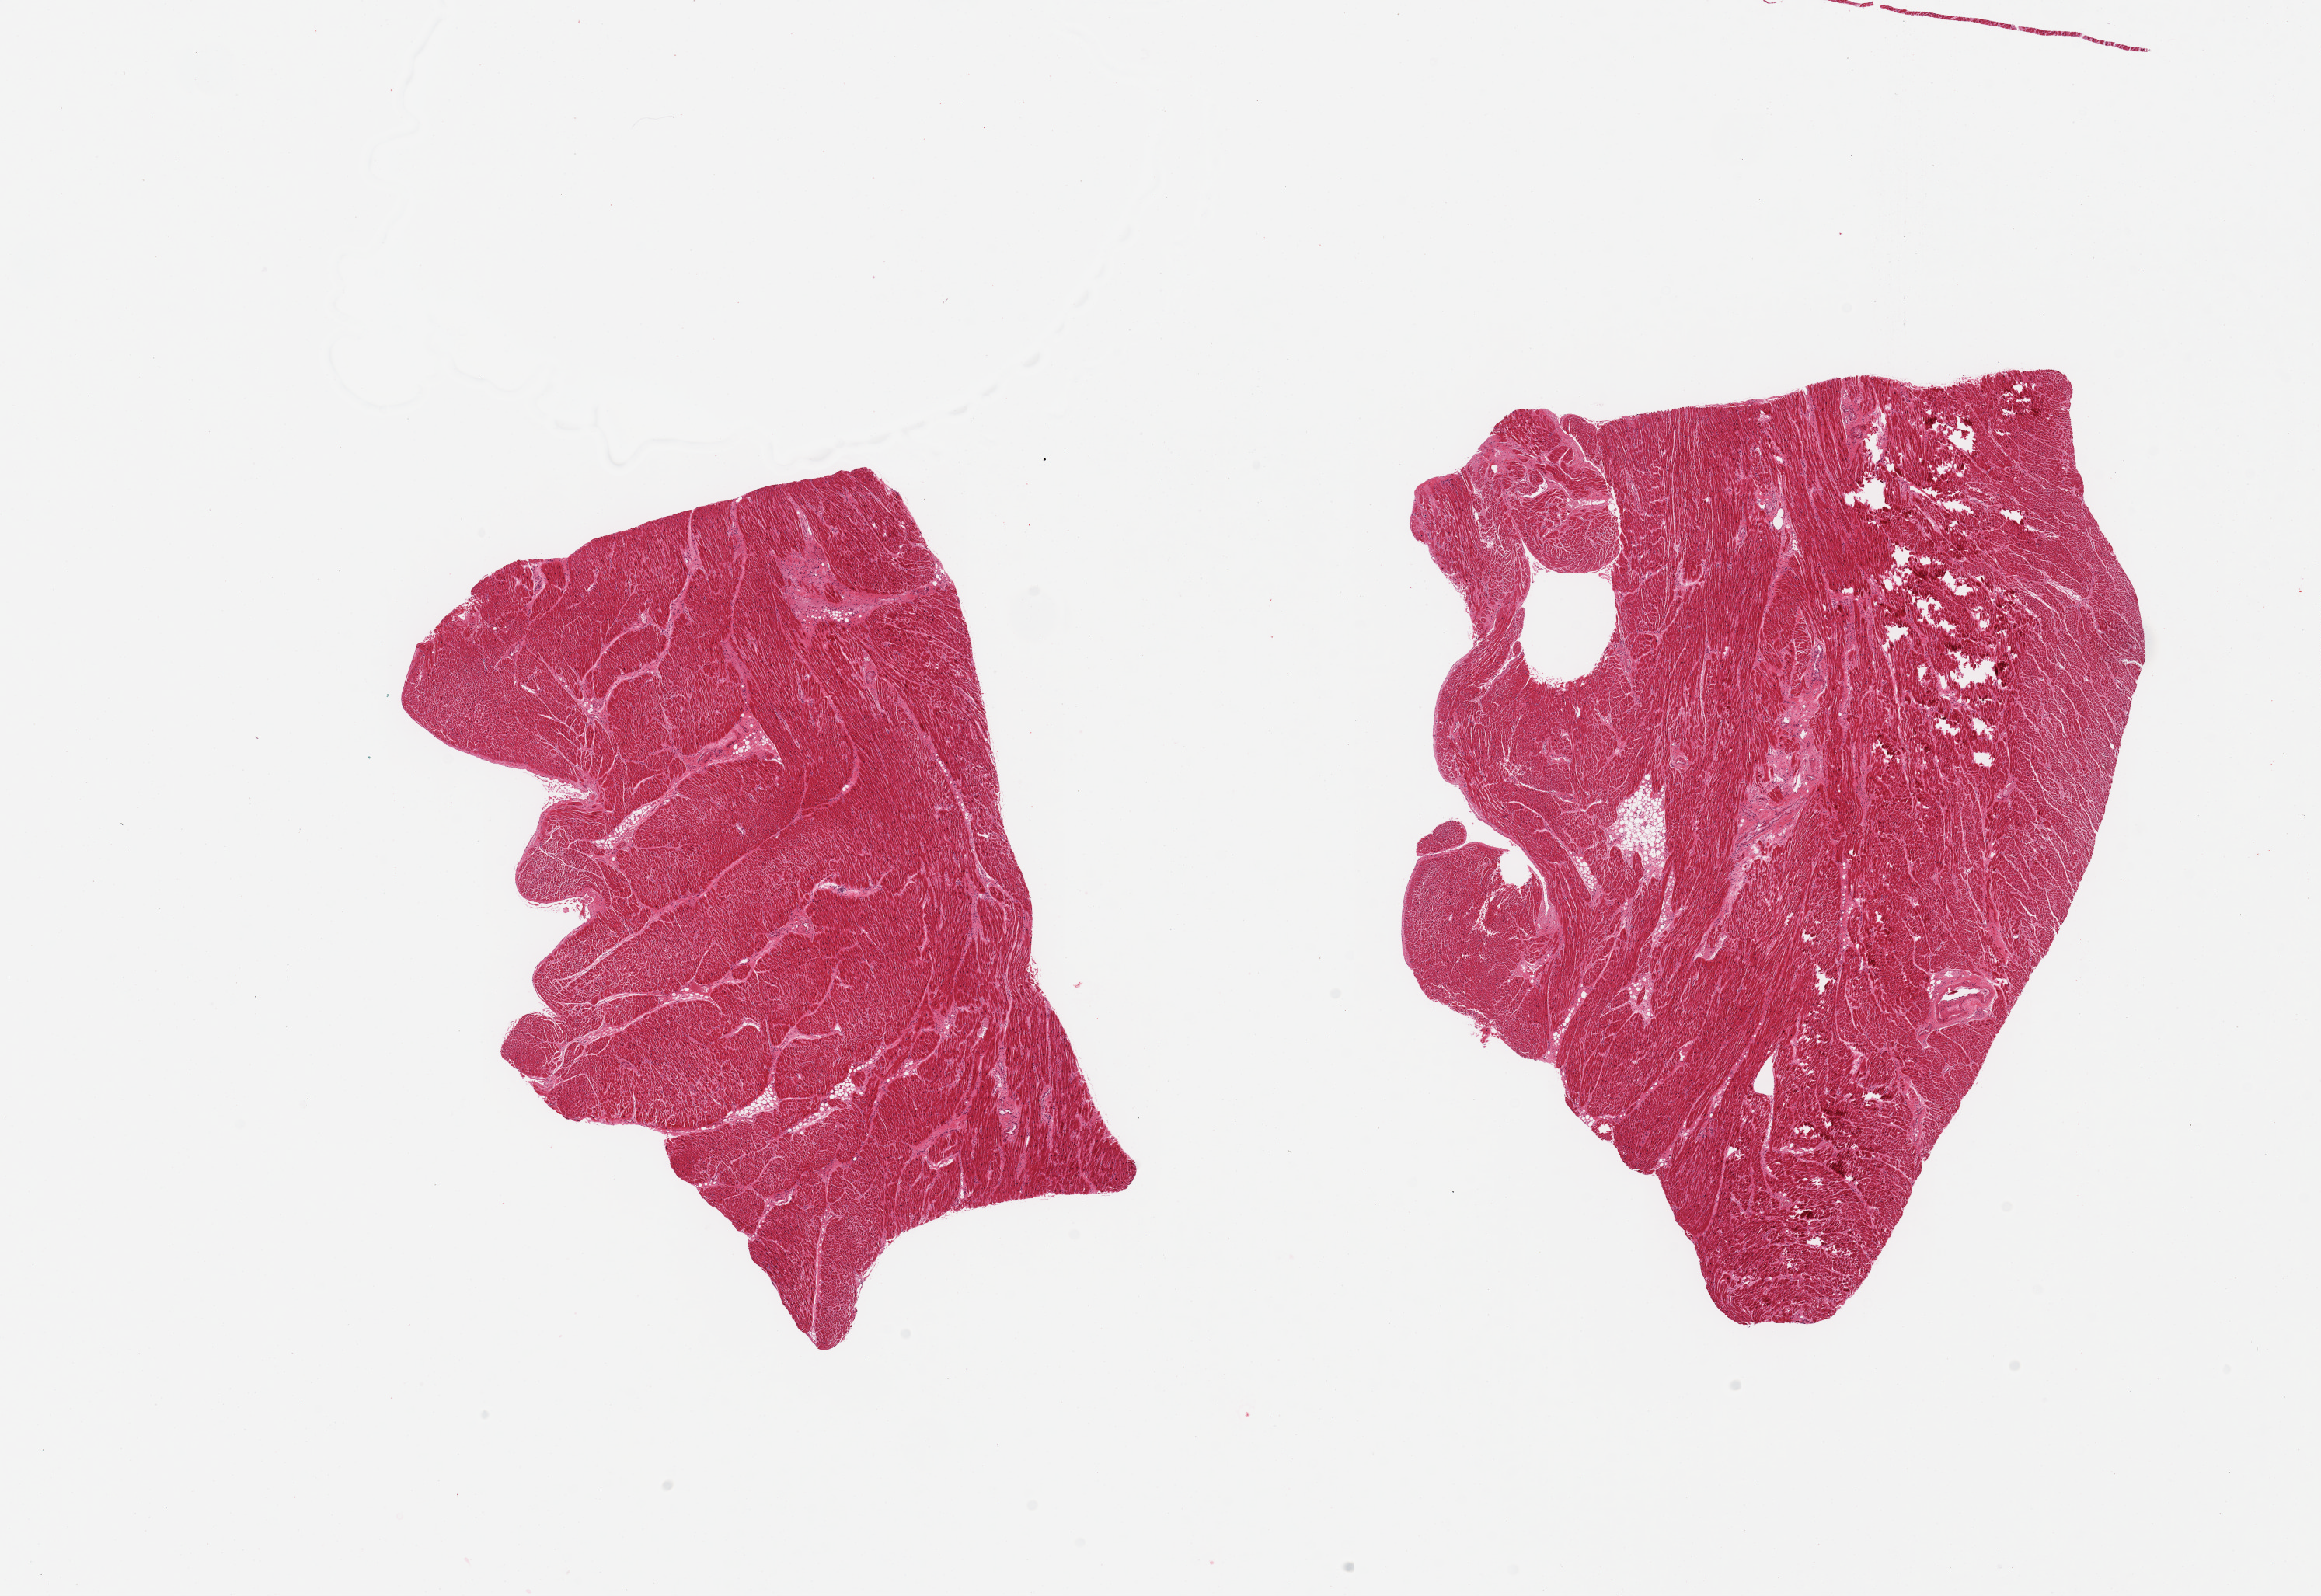
H&E whole-slide image, brightfield, low-resolution overview of the scanned area, about 23.6 x 16.2 mm (acquisition: 20x scan), PAXgene-fixed paraffin-embedded (PFPE) section, section of heart (target tissue), donor tissue sample.
Review note (as recorded): 2 pieces.